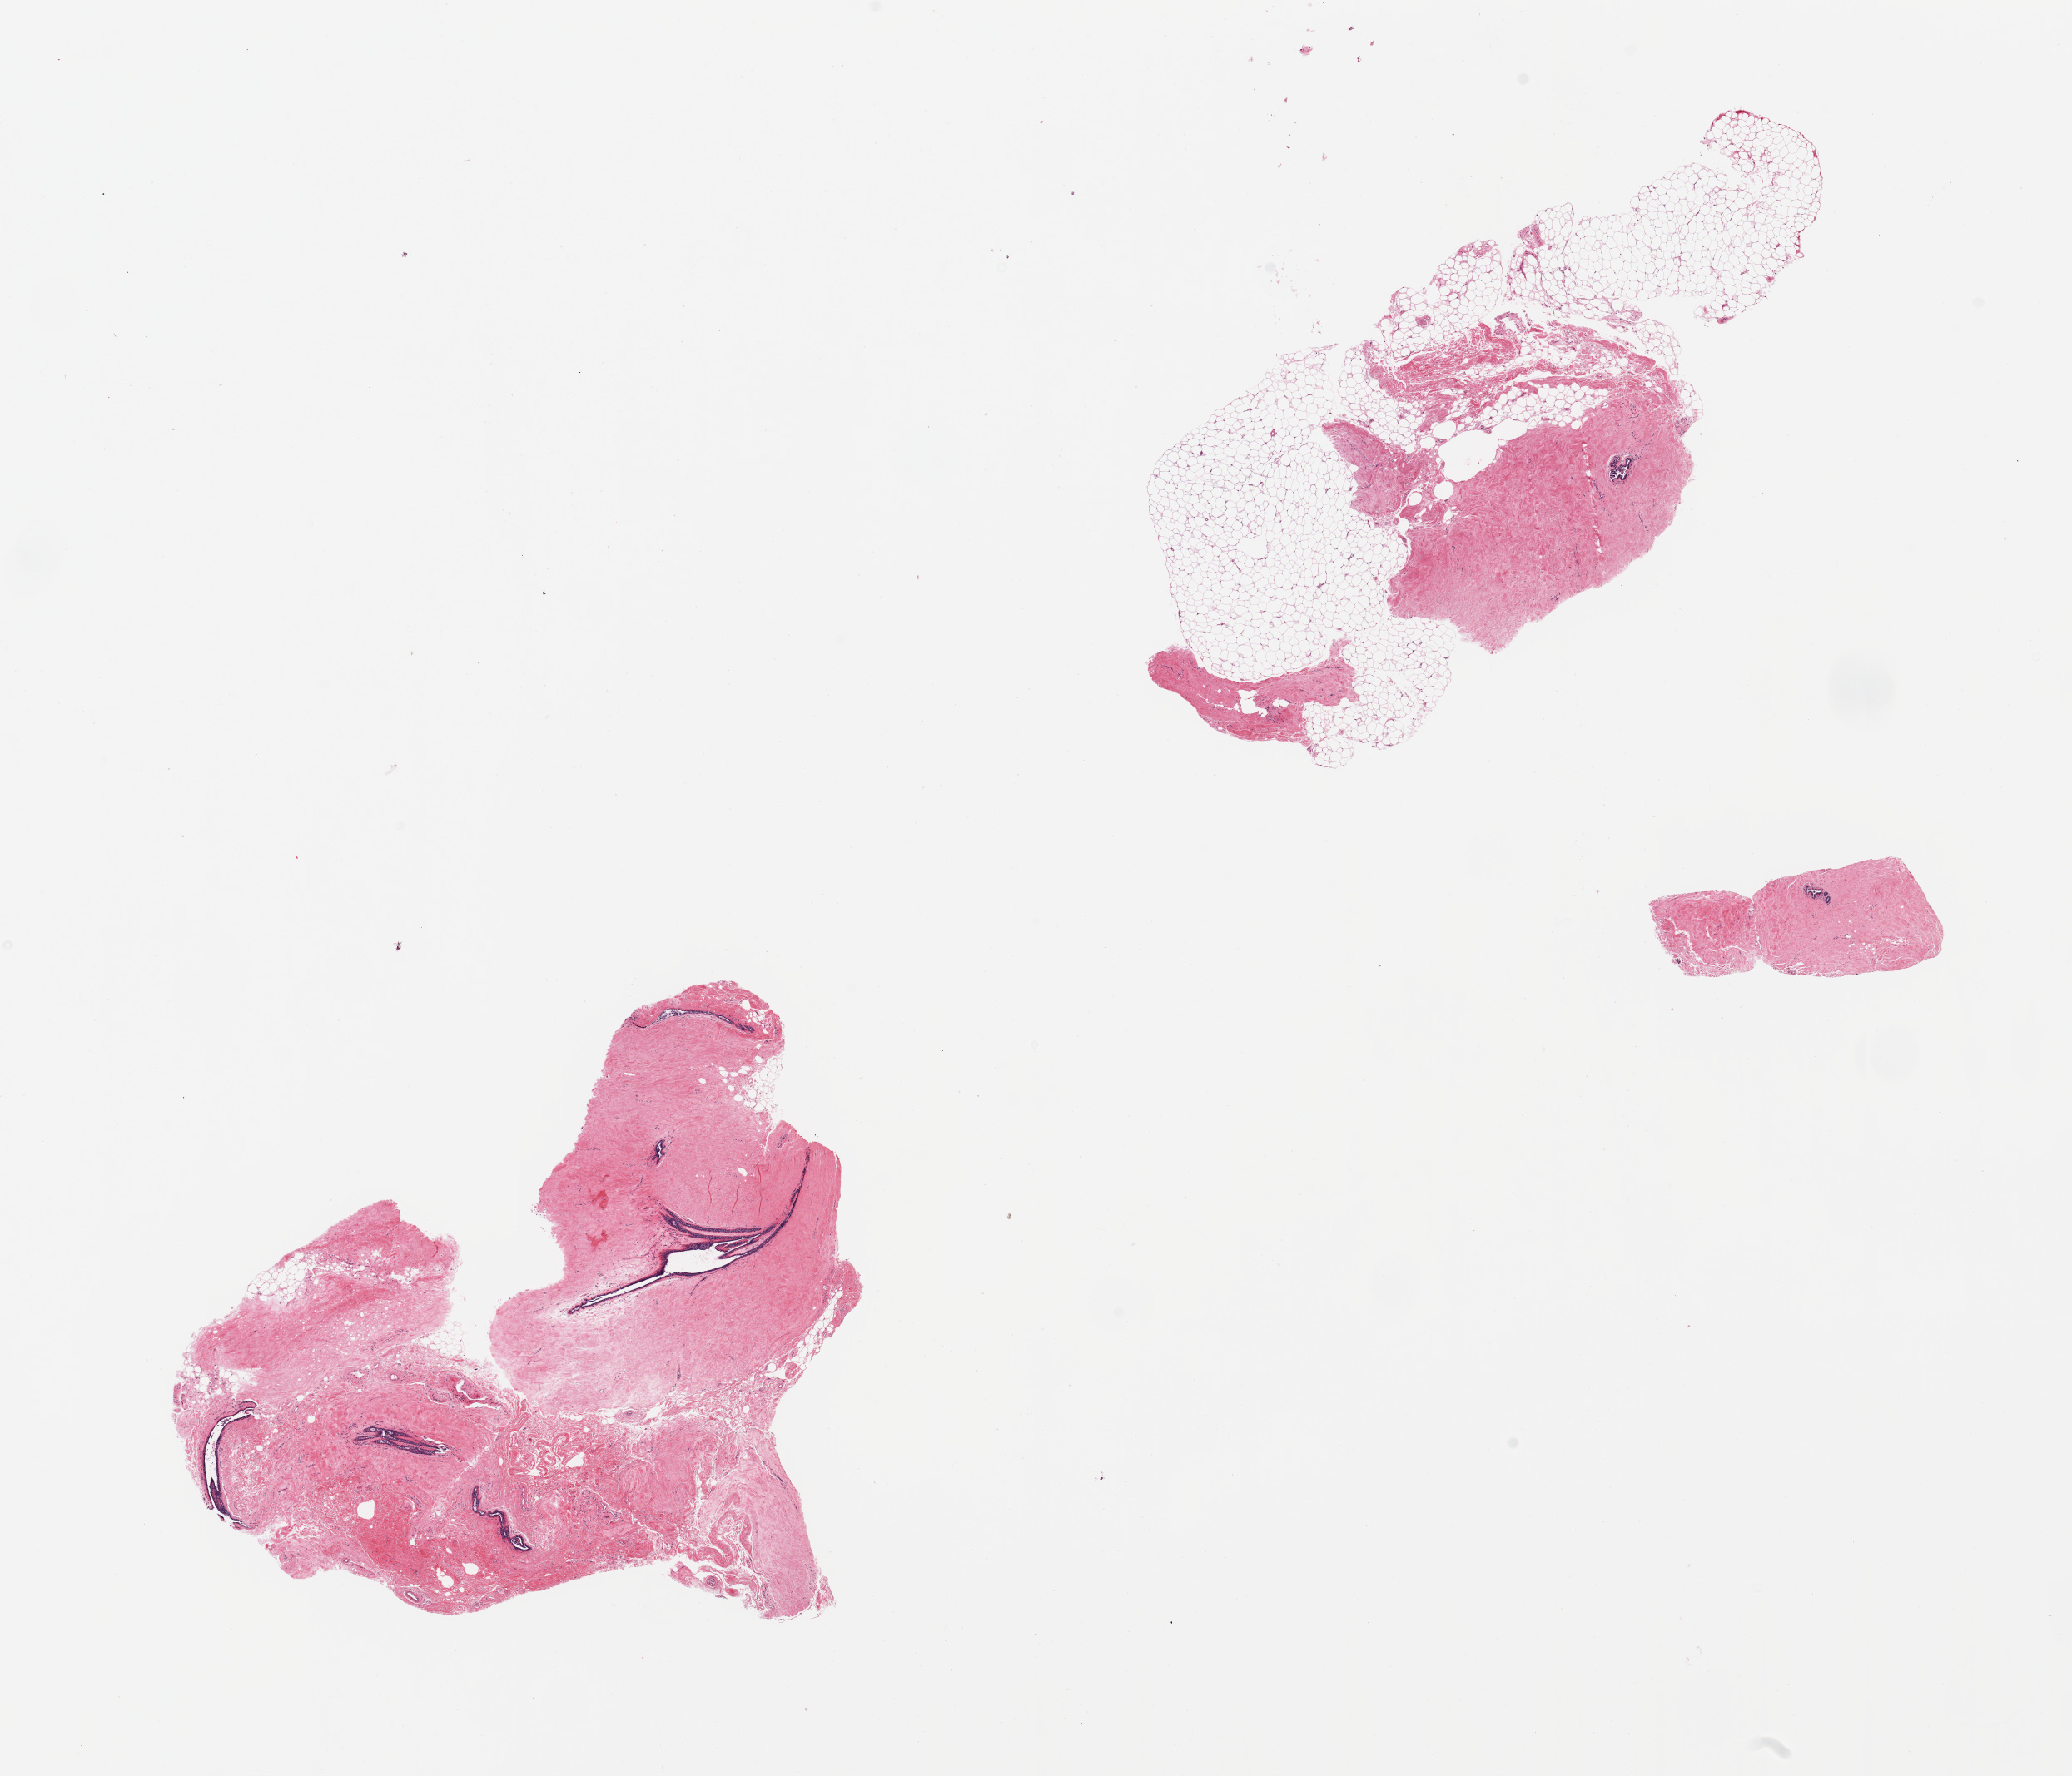
Digitized H&E-stained section — low-resolution overview of the scanned area, about 19.7 x 16.9 mm, PAXgene-fixed, paraffin-embedded tissue, target tissue: breast, donor tissue sample. Male donor.
Pathologist's review note for this sample: 2 pieces sromal and (focal) ductal gynecomastoid hyperplasia.